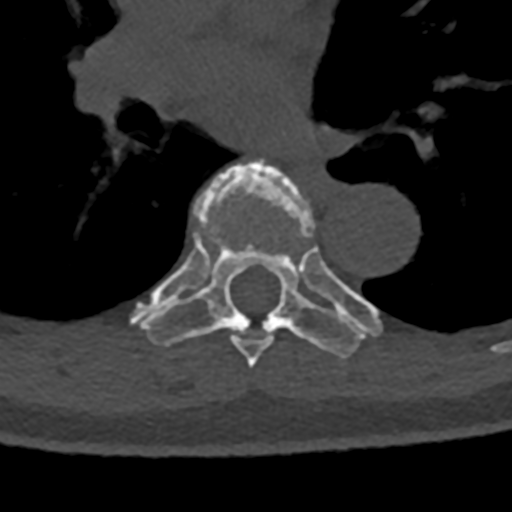
CT including the spine, one axial slice; position 779 of 797 along the scan axis; reconstruction kernel Br40s/3; 120 kVp; bone window (W 1800 / L 400 HU); 0.5 mm slice thickness; 512 × 512 image matrix. Male patient, age 74 years. From the clinical record (not read from this slice): primary cancer: renal; vertebrae with lytic lesions (as recorded): T10, L1, L2, L3, L4, L5.
Annotated regions visible in this slice (semi-automatically segmented with operator editing):
- T6 vertebra: box from (x=173, y=162) to (x=315, y=368) px
- T7 vertebra: (x=131, y=206)–(x=381, y=358)